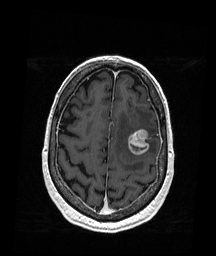
Brain MRI from a brain-tumour surgery series, one axial slice. Position 51 of 176 along the scan axis. T1-weighted post-contrast. 1 mm slice thickness. 216 × 256 image matrix, field of view 211 × 250 mm. Case-level facts recorded for this patient, not image findings: histopathology: Metastatic Melanoma; tumour location: Left Frontal.
Annotated regions visible in this slice (manually delineated by an expert):
- tumour: box from (x=127, y=128) to (x=149, y=156) px